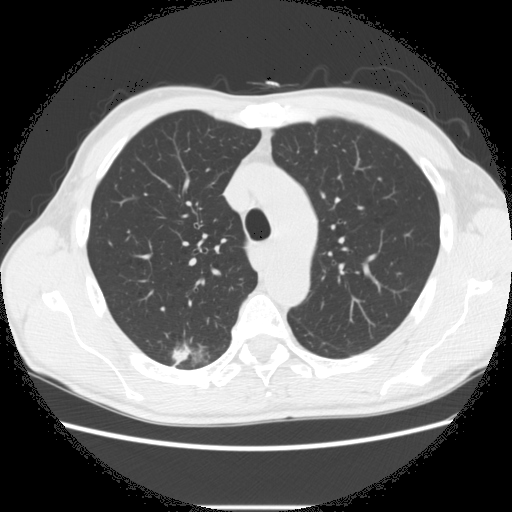
Low-dose screening chest CT, axial slice, second annual screen, lung window (W 1500 / L -600 HU), 2.5 mm slice thickness, slice 77 of 282 in the series, 512 × 512 image matrix, field of view 360 × 360 mm. Male participant, aged 66 years at enrolment.
• Expert-annotated lung lesion, box from (x=161, y=338) to (x=221, y=375) px.
• The screening reader recorded 5 non-calcified nodules or masses ≥4 mm on this exam (right lower lobe, right upper lobe, right upper lobe, right upper lobe, left lower lobe); which of them this box marks is not recorded.
• Lung cancer was diagnosed 75 days after this screen: adenocarcinoma, NOS, right upper lobe, undifferentiated (G4), stage IA (AJCC 6th edition), 20 mm at pathology.